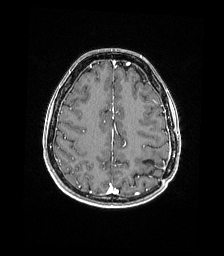
Brain MRI from a brain-tumour surgery series, one axial slice; position 56 of 176 along the scan axis; T1-weighted post-contrast; 224 × 256 image matrix, field of view 224 × 256 mm. Case-level facts recorded for this patient, not image findings: histopathology: Atypical meningioma; WHO grade: 2; tumour location: Paramedian Left Parietal.
Structures marked on this image (expert manual segmentation):
- previous resection cavity: bounding box (x1, y1, x2, y2) in pixels: (144, 160, 155, 165)